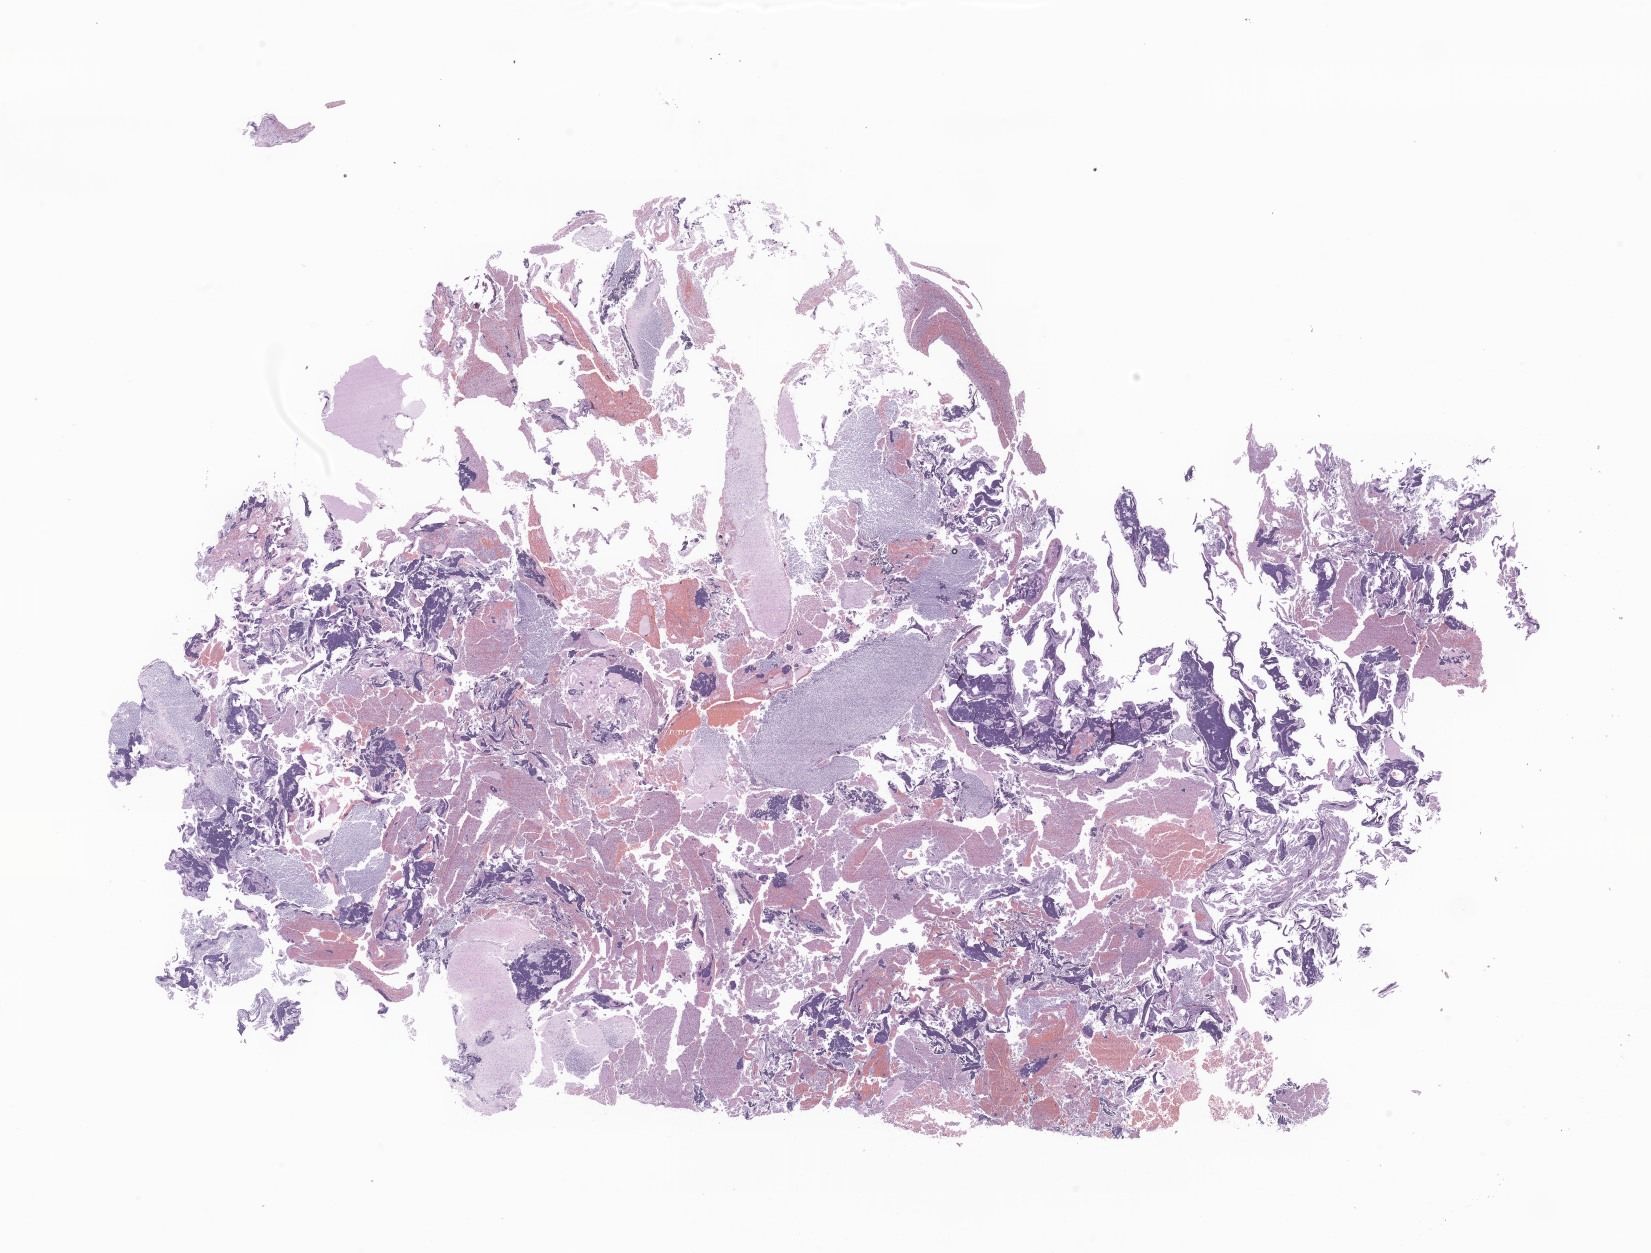
Whole-slide image, H&E stain of tumor tissue from the brain — whole scanned area (about 27.8 x 21.1 mm) shown as a low-resolution overview. Formalin-fixed paraffin-embedded section. Female patient, age 98 months (8 years 2 months).
Diagnosis: Neoplasm, uncertain whether benign or malignant.